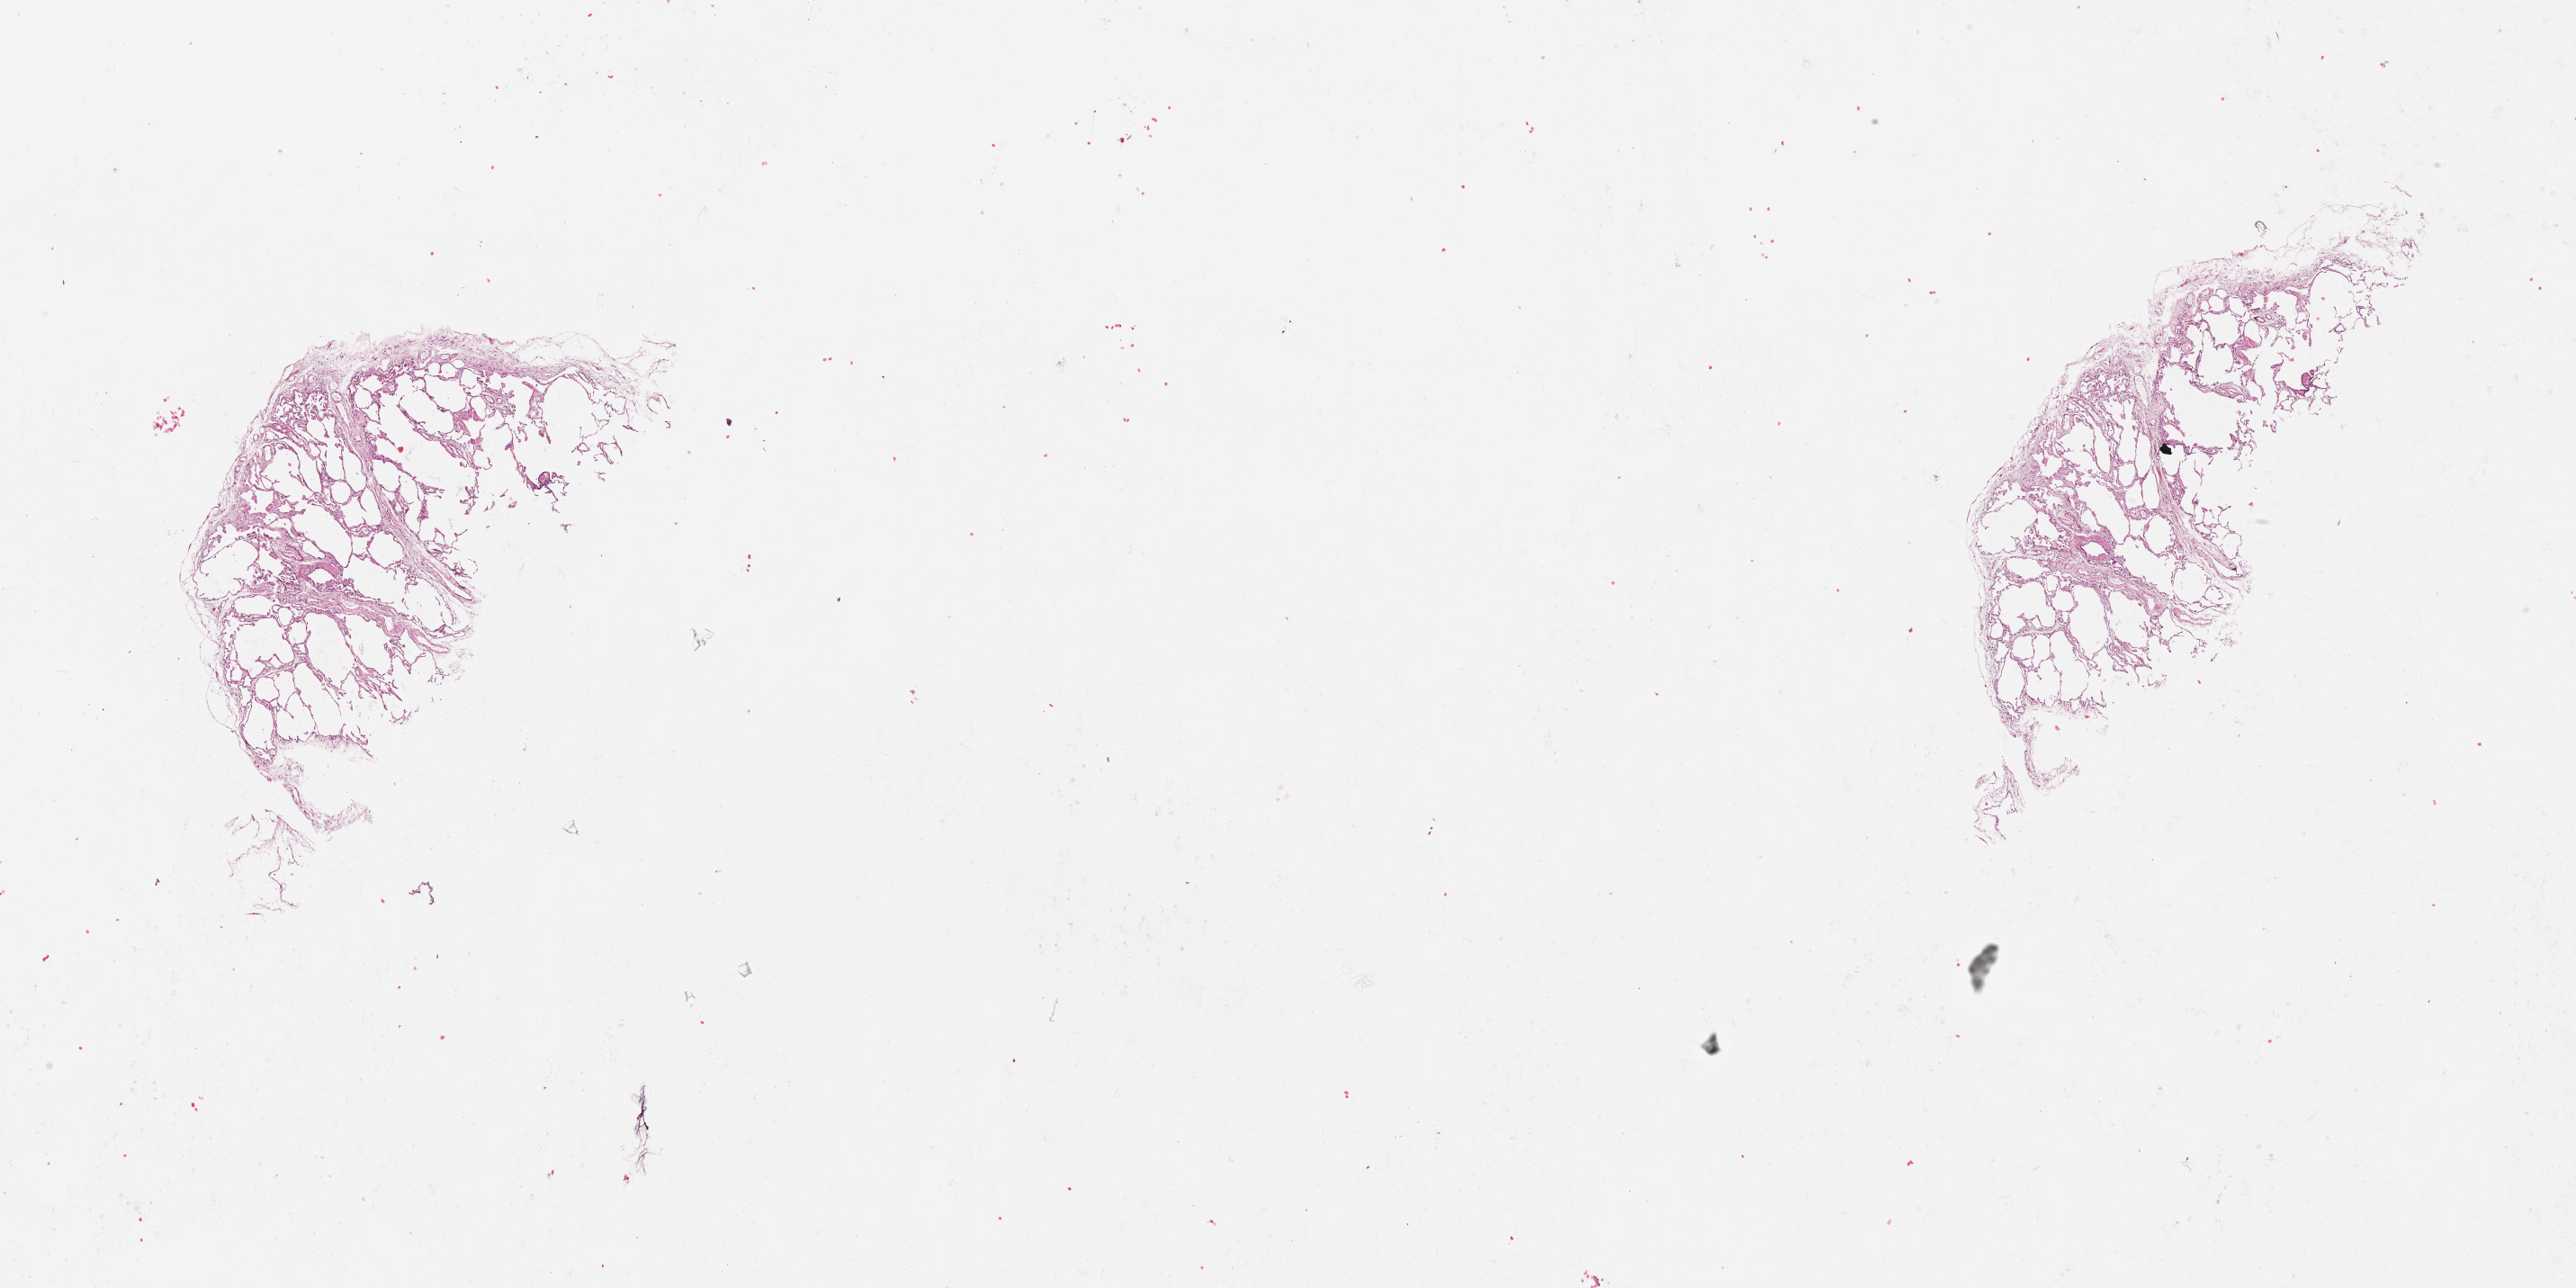
Digitized H&E-stained tissue section (whole slide), shown as a low-resolution overview of the whole scanned area (about 23.1 x 11.5 mm, from a 20x scan). Normal (non-tumour) tissue sample, lung. 74-year-old female patient.
This section: normal (non-tumour) tissue from the same patient. Patient diagnosis (cohort enrolment): squamous cell carcinoma (lung).